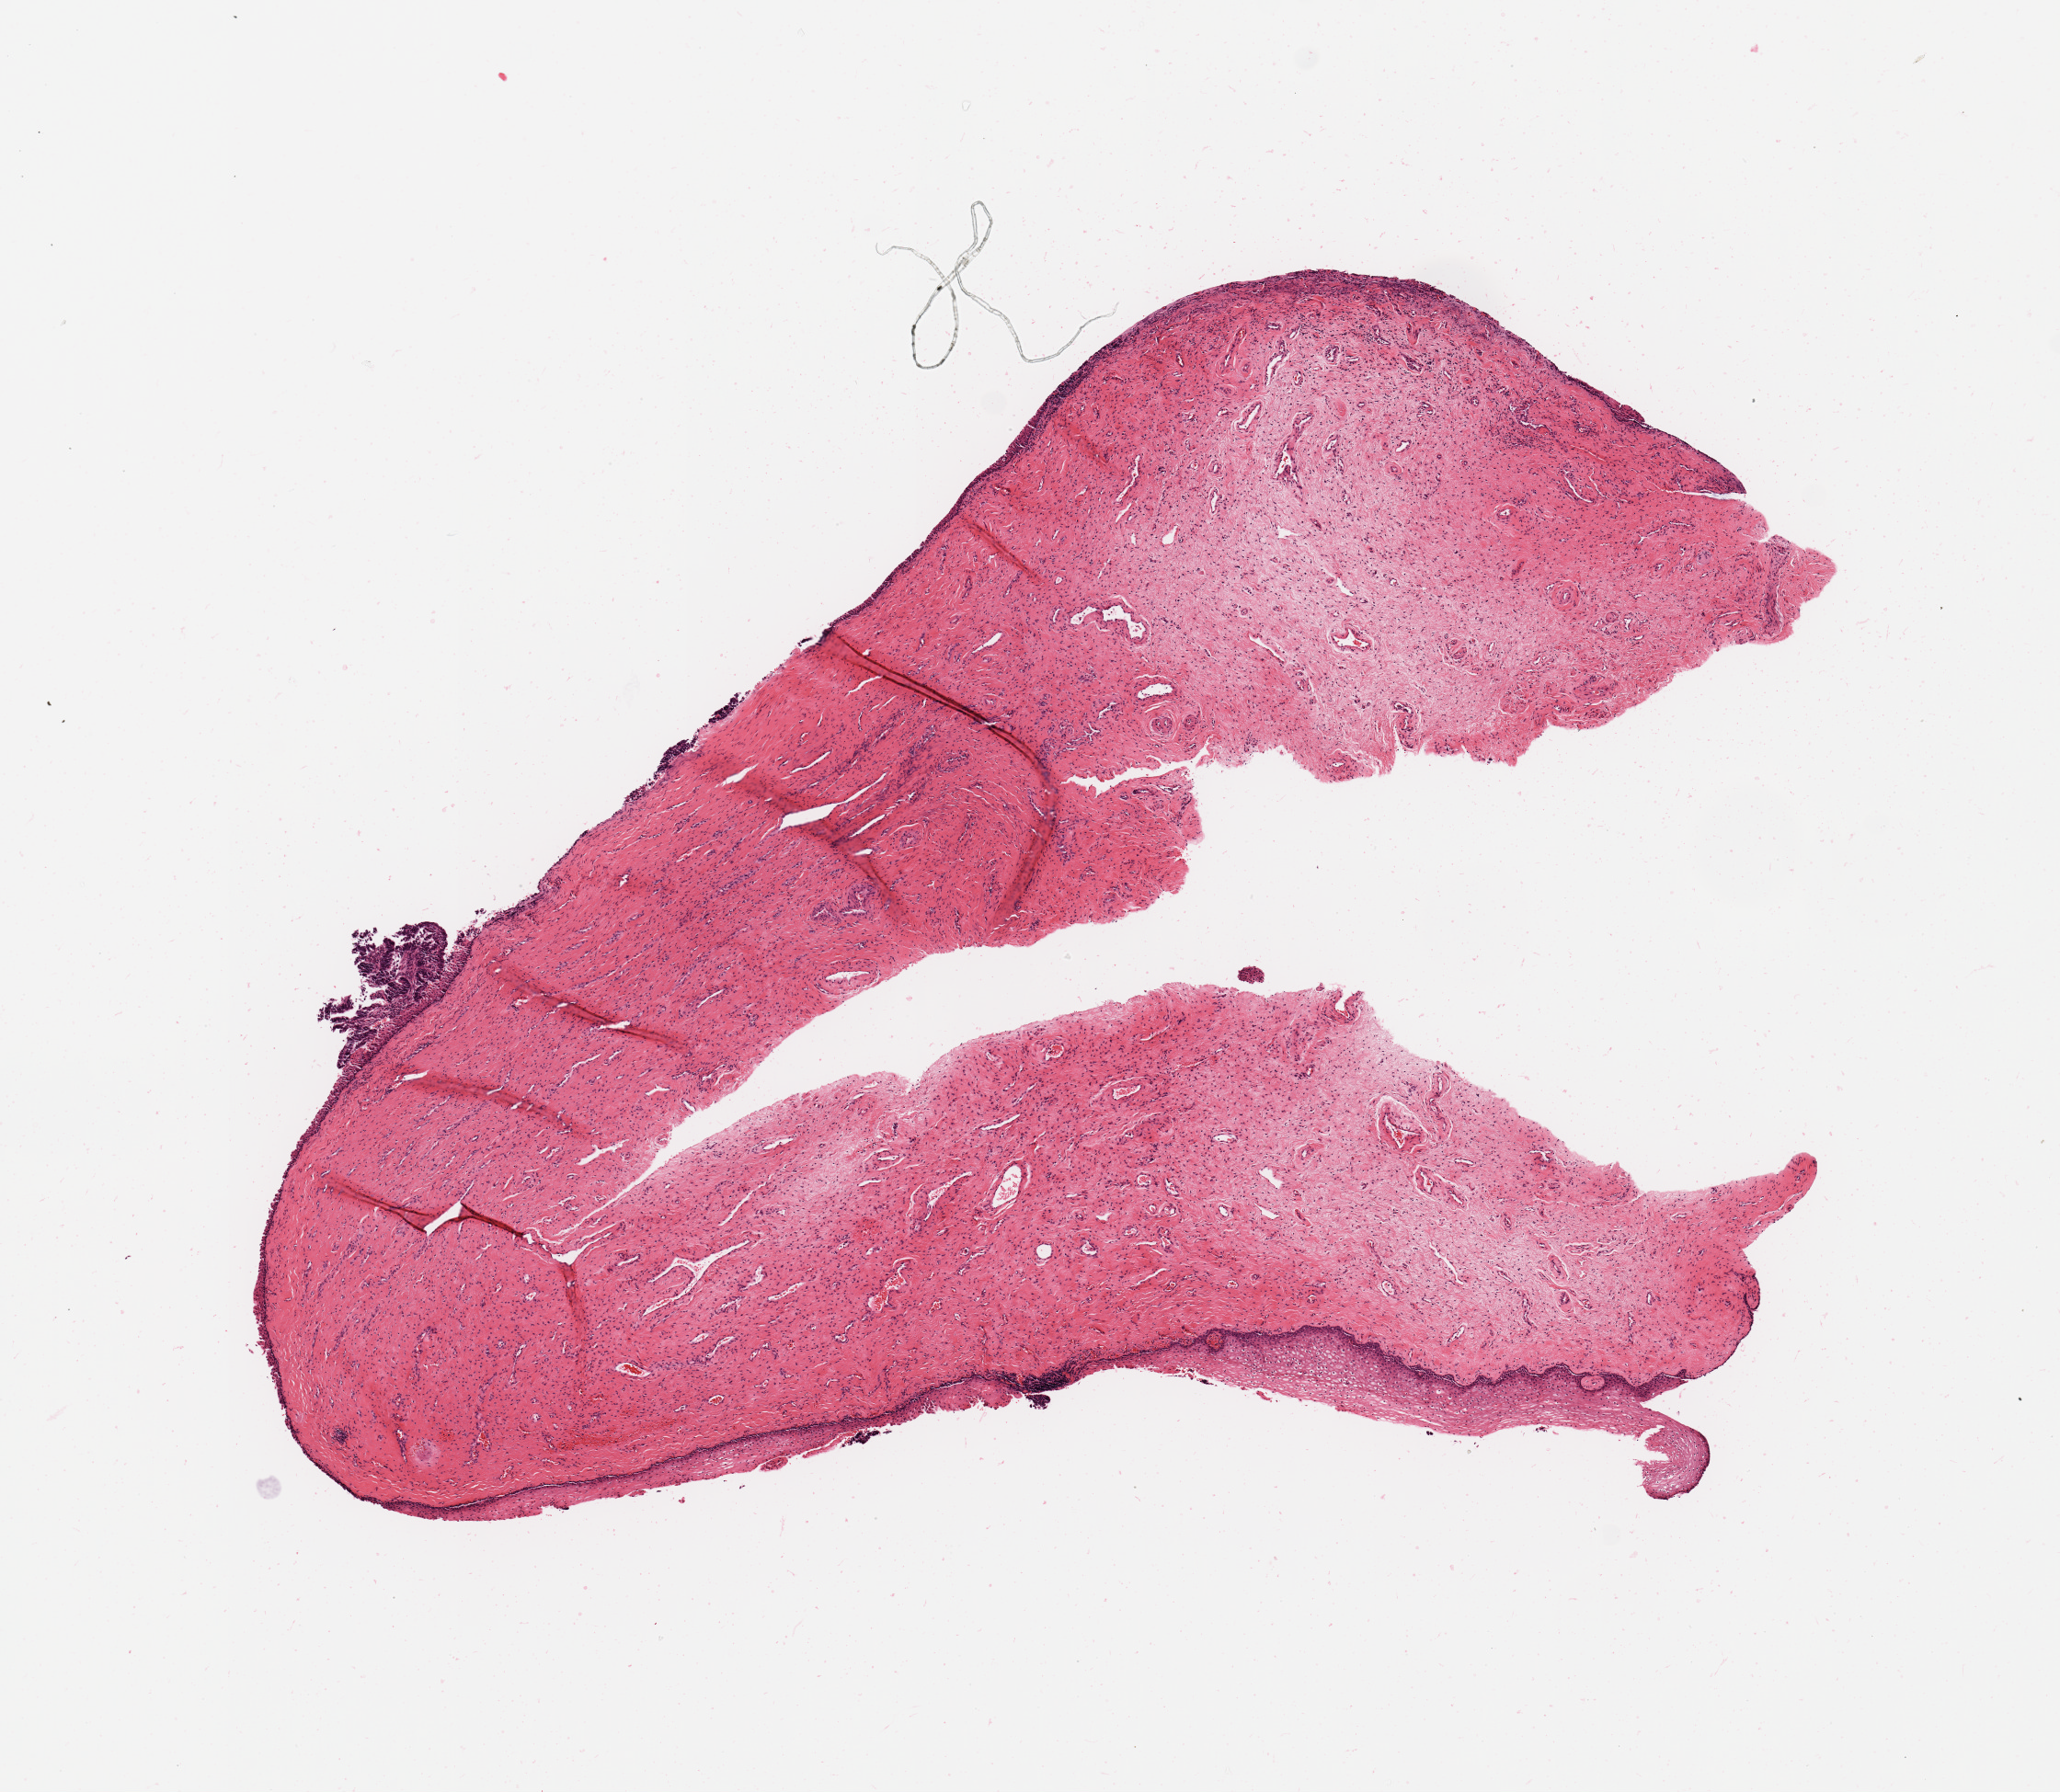
Digitized Hematoxylin and eosin (H&E) stained tissue section (whole slide) — shown as a low-resolution overview of the whole scanned area (about 8.9 x 7.7 mm, from a 20x scan); uterus, normal (non-tumour) tissue. 66-year-old female patient.
• this section: normal (non-tumour) tissue from the same patient
• patient diagnosis: Endometrioid adenocarcinoma, NOS